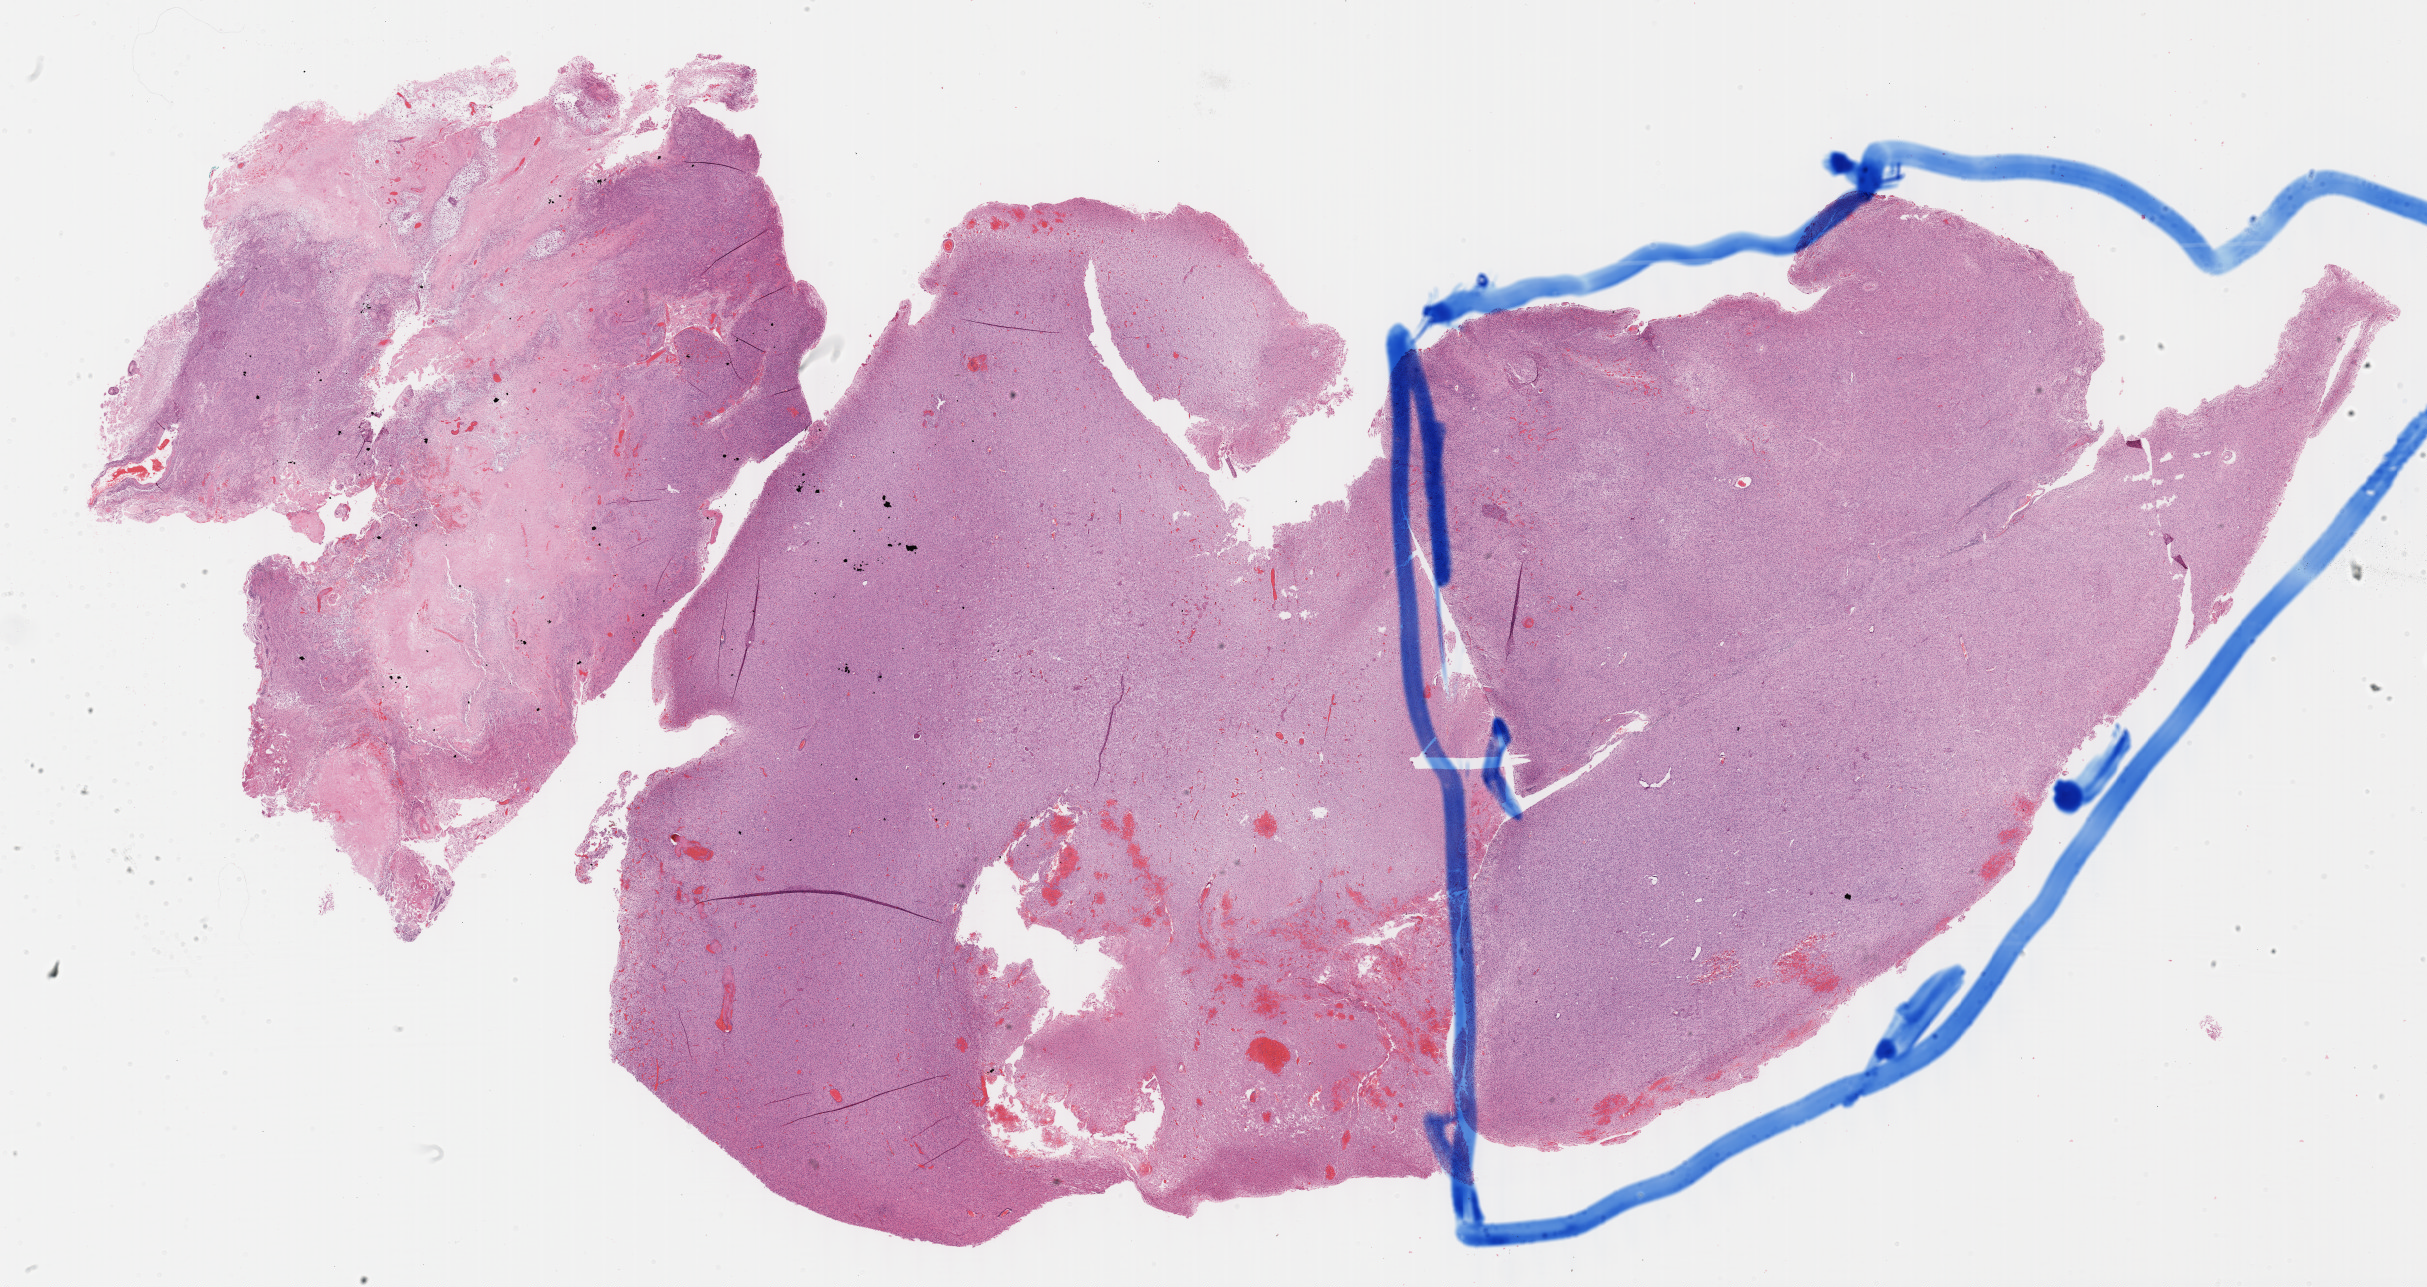
Whole-slide histology image, H&E-stained — low-resolution overview of the scanned area, about 39.2 x 20.8 mm (slide scanned at 40x); formalin-fixed paraffin-embedded (FFPE) diagnostic section; primary tumour sample from the brain. Female, age 57 years at initial diagnosis.
- diagnosis: Glioblastoma